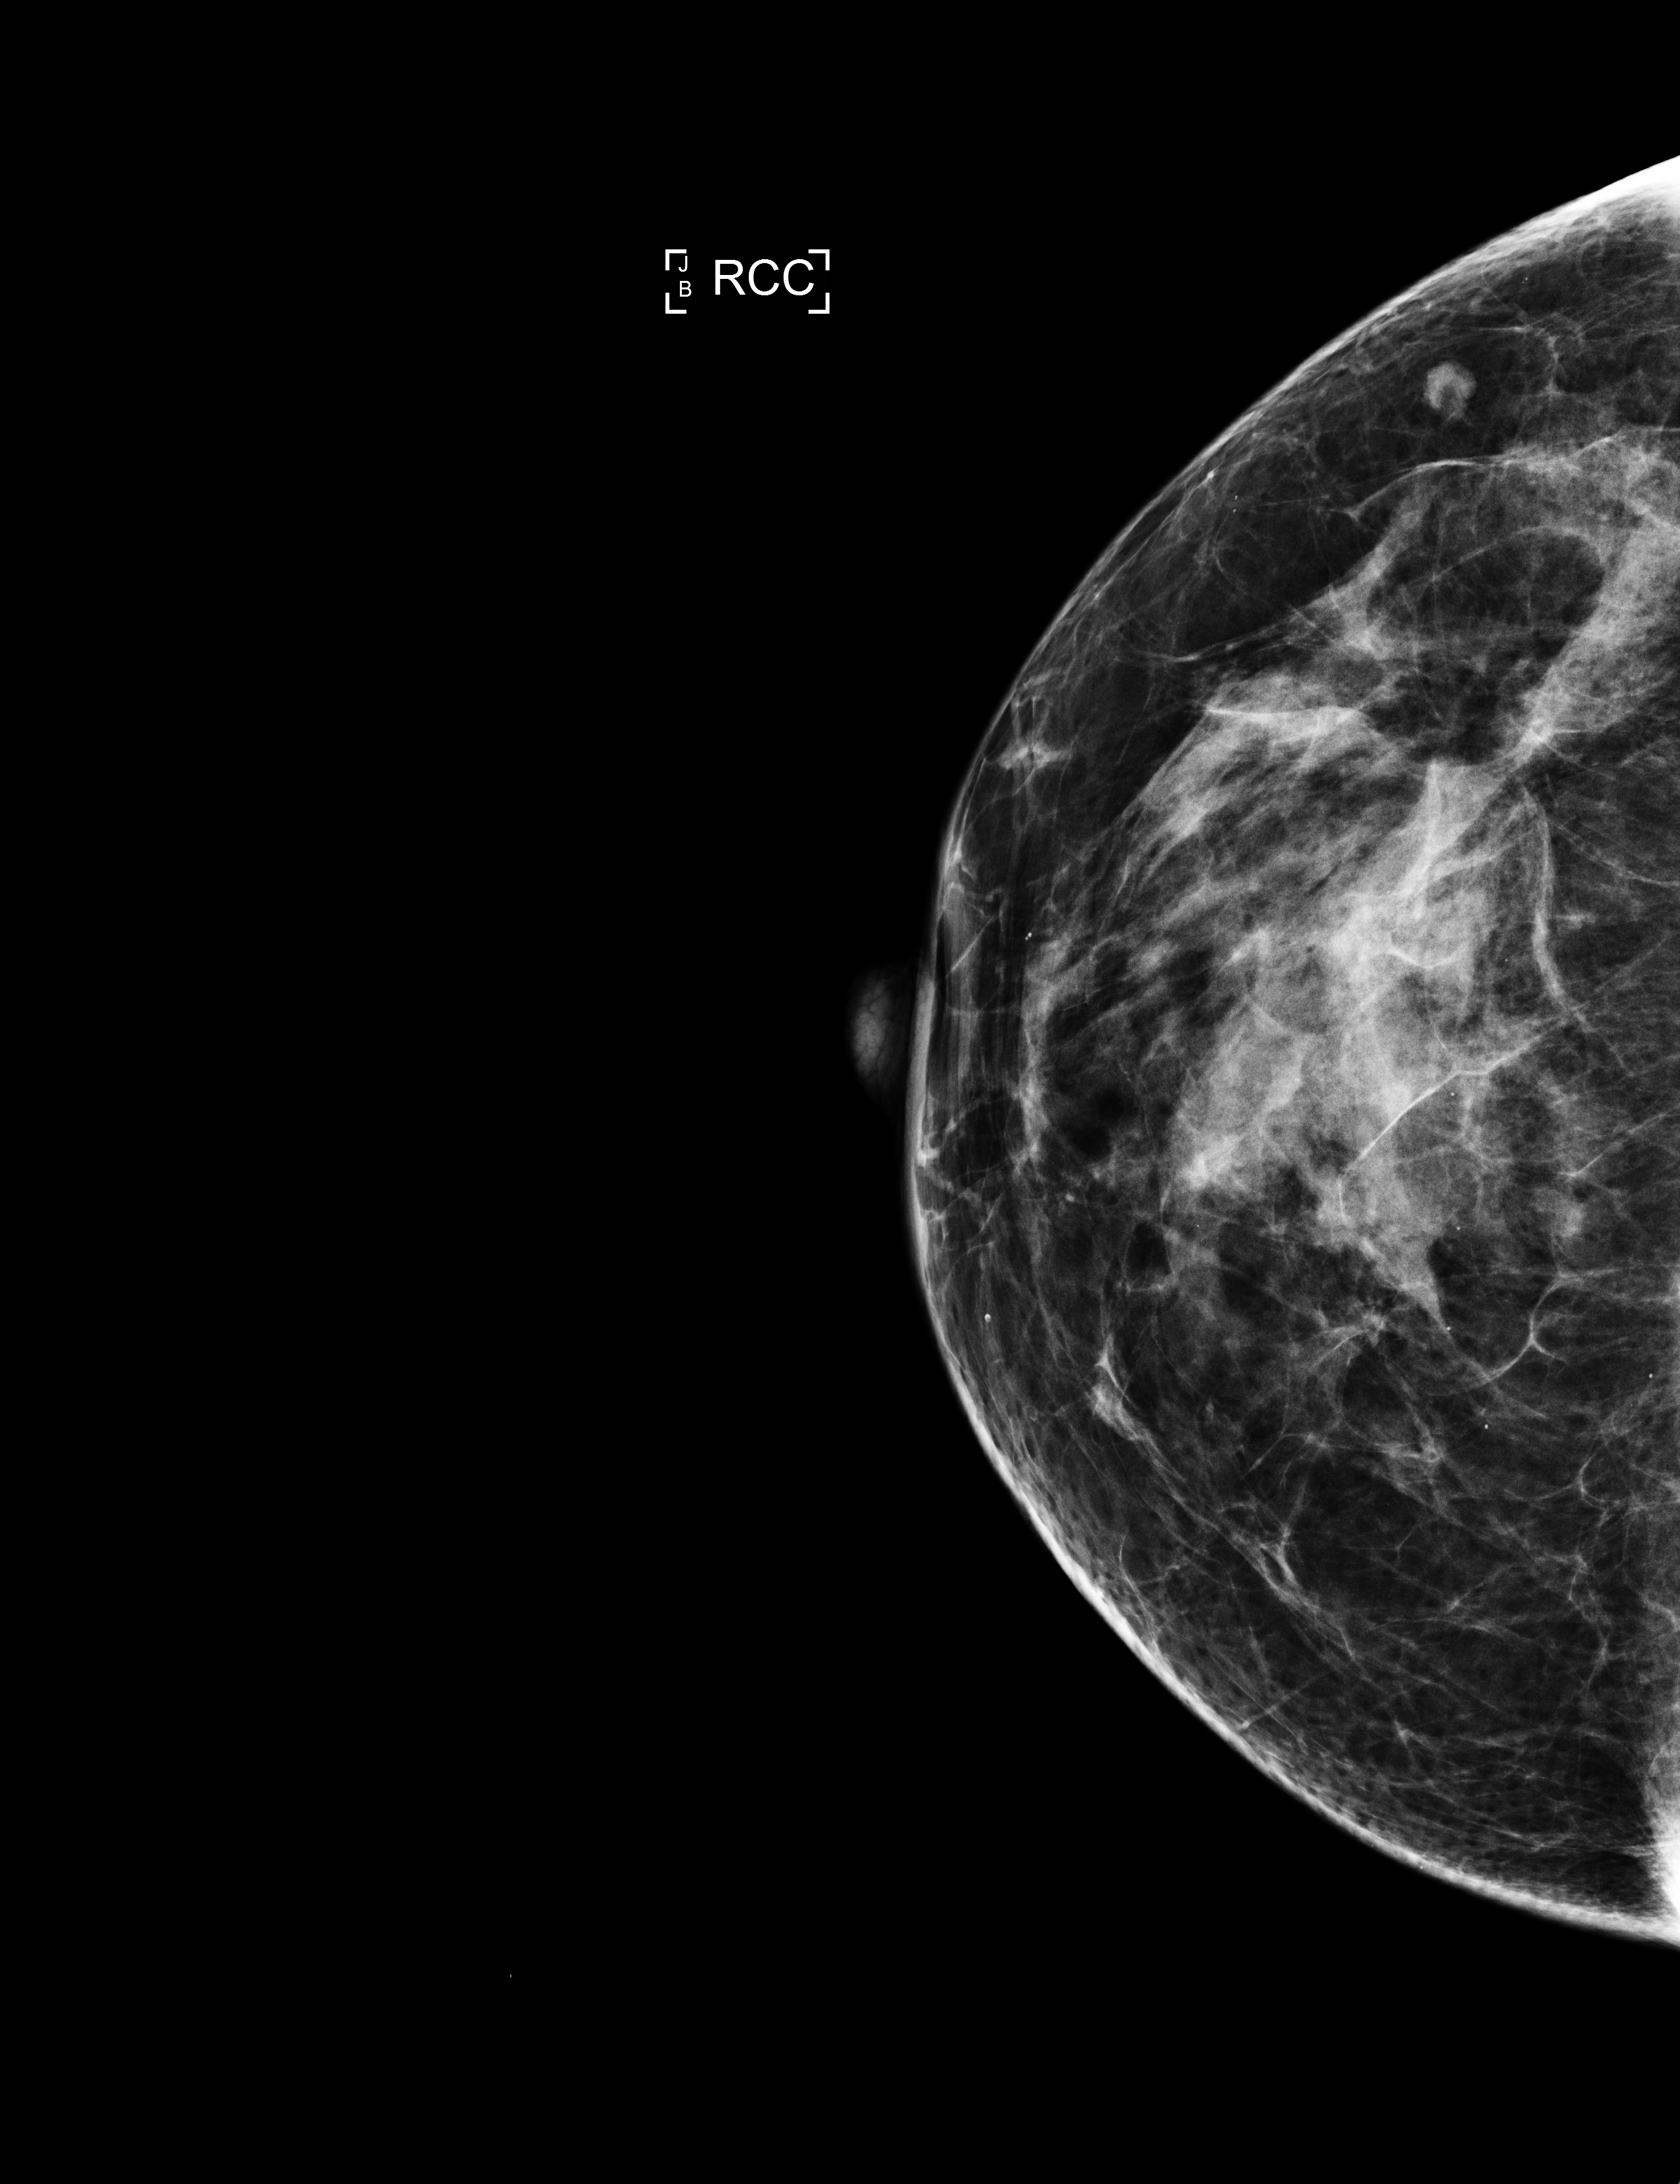
Annual screening mammography examination; compressed breast thickness 52 mm; system: Selenia Dimensions. Patient: female, 61 years.
Image type: full-field digital mammogram. Breast: right. Projection: craniocaudal (CC) view.